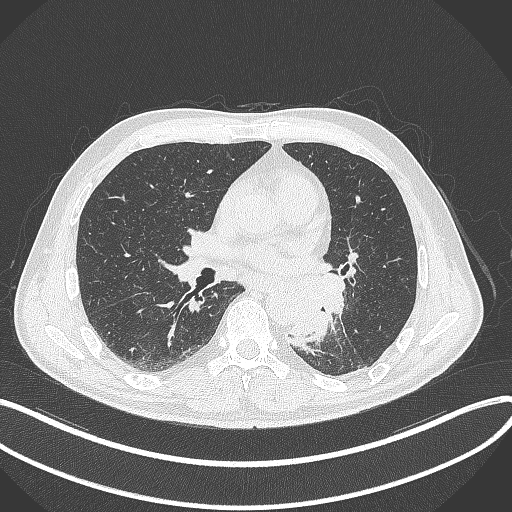
Chest CT, one axial slice; reconstruction kernel B70f; 120 kVp; lung window (W 1500 / L -600 HU); 1 mm slice thickness; 512 × 512 image matrix, field of view 400 × 400 mm. Patient: male, 59 years. Case-level facts recorded for this patient, not image findings: clinical TNM (as recorded): T2a N2 M0.
Outlined on this slice (rectangle marked by the reading radiologist):
- lung tumour (recorded histology: squamous cell carcinoma): bounding box [x1, y1, x2, y2] px = [301, 272, 346, 346]